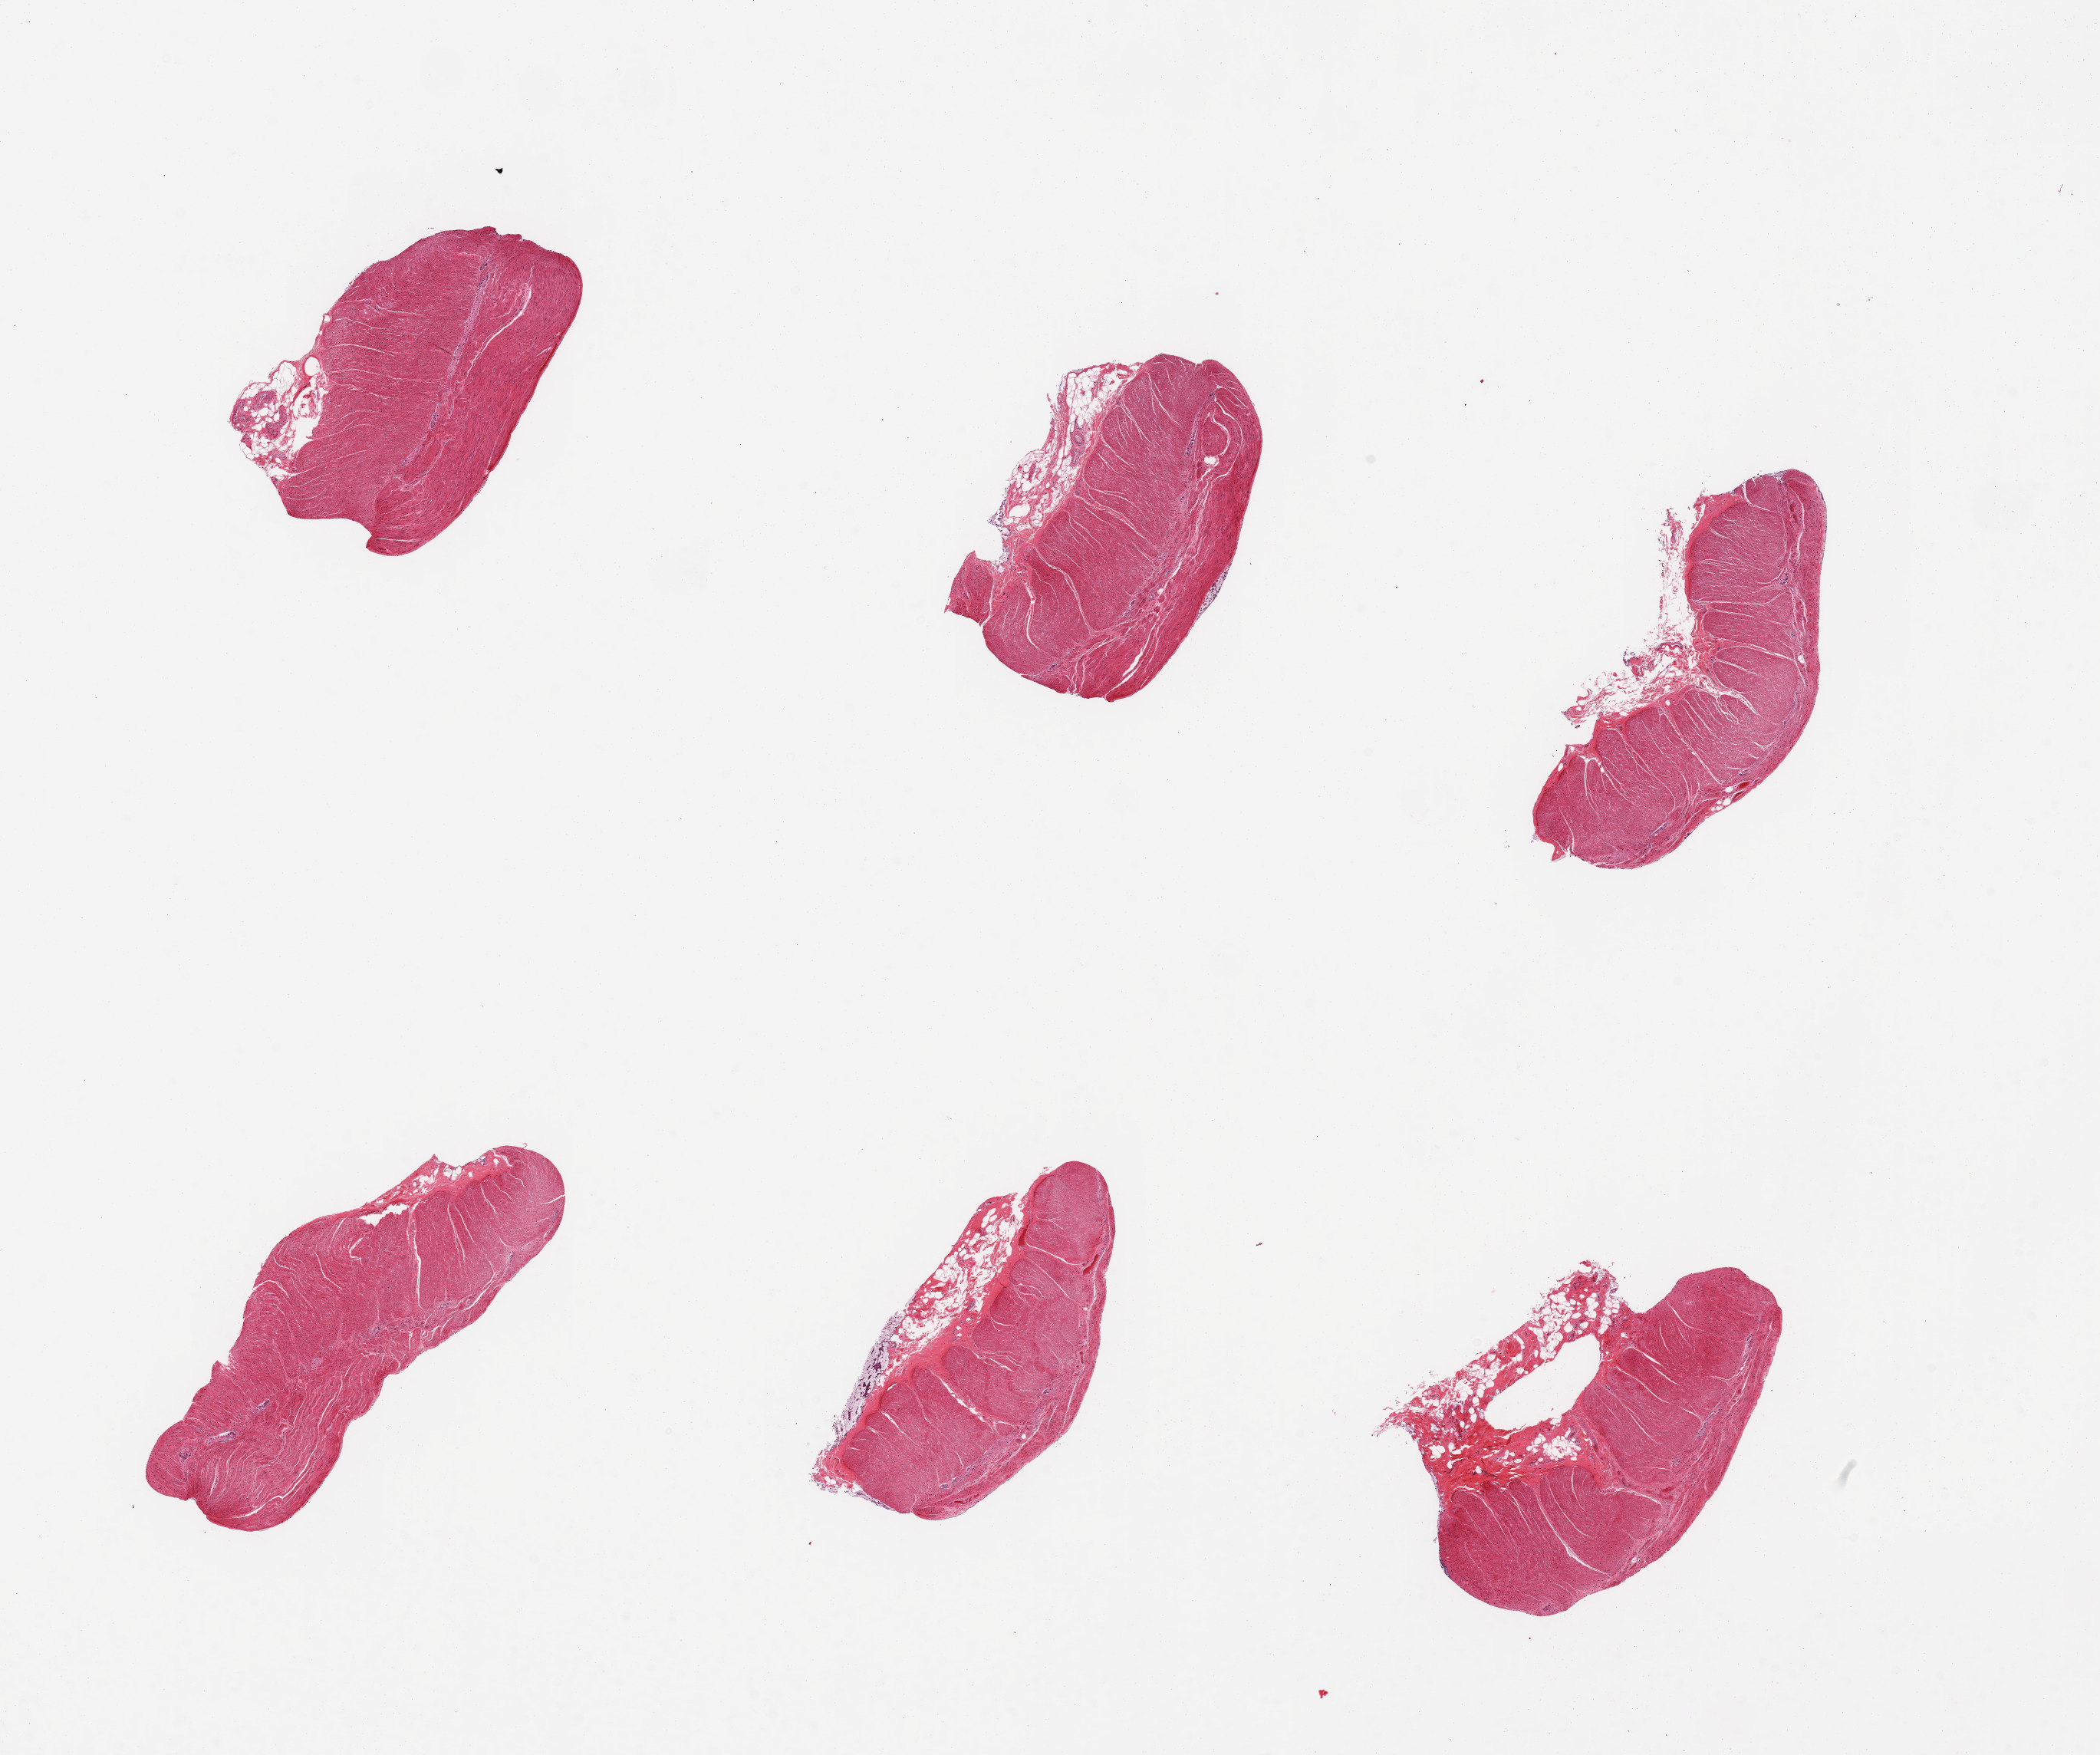
H&E whole-slide image, brightfield, shown as a low-resolution overview of the whole scanned area (about 21.7 x 18.1 mm); PAXgene-fixed, paraffin-embedded tissue; target tissue: sigmoid colon; tissue donor sample. Male donor.
* pathologist's review note for this sample: 6 pieces; submucosal fat on 5 of 6 pieces measuring up to 1 mm thick; autolyzed mucosal remnant